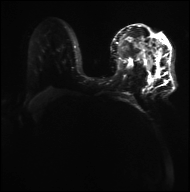
Breast MRI, one axial slice. Position 19 of 36 along the scan axis. Diffusion-weighted series; image 2 of 4 stored at this slice position (different b-values; order by instance number). 3 T. 4 mm slice thickness. 190 × 192 image matrix, field of view 317 × 320 mm. Female patient.
Outlined on this slice (expert manual segmentation):
- tumour on diffusion-weighted imaging: bounding box [x1, y1, x2, y2] px = [4, 56, 39, 78]